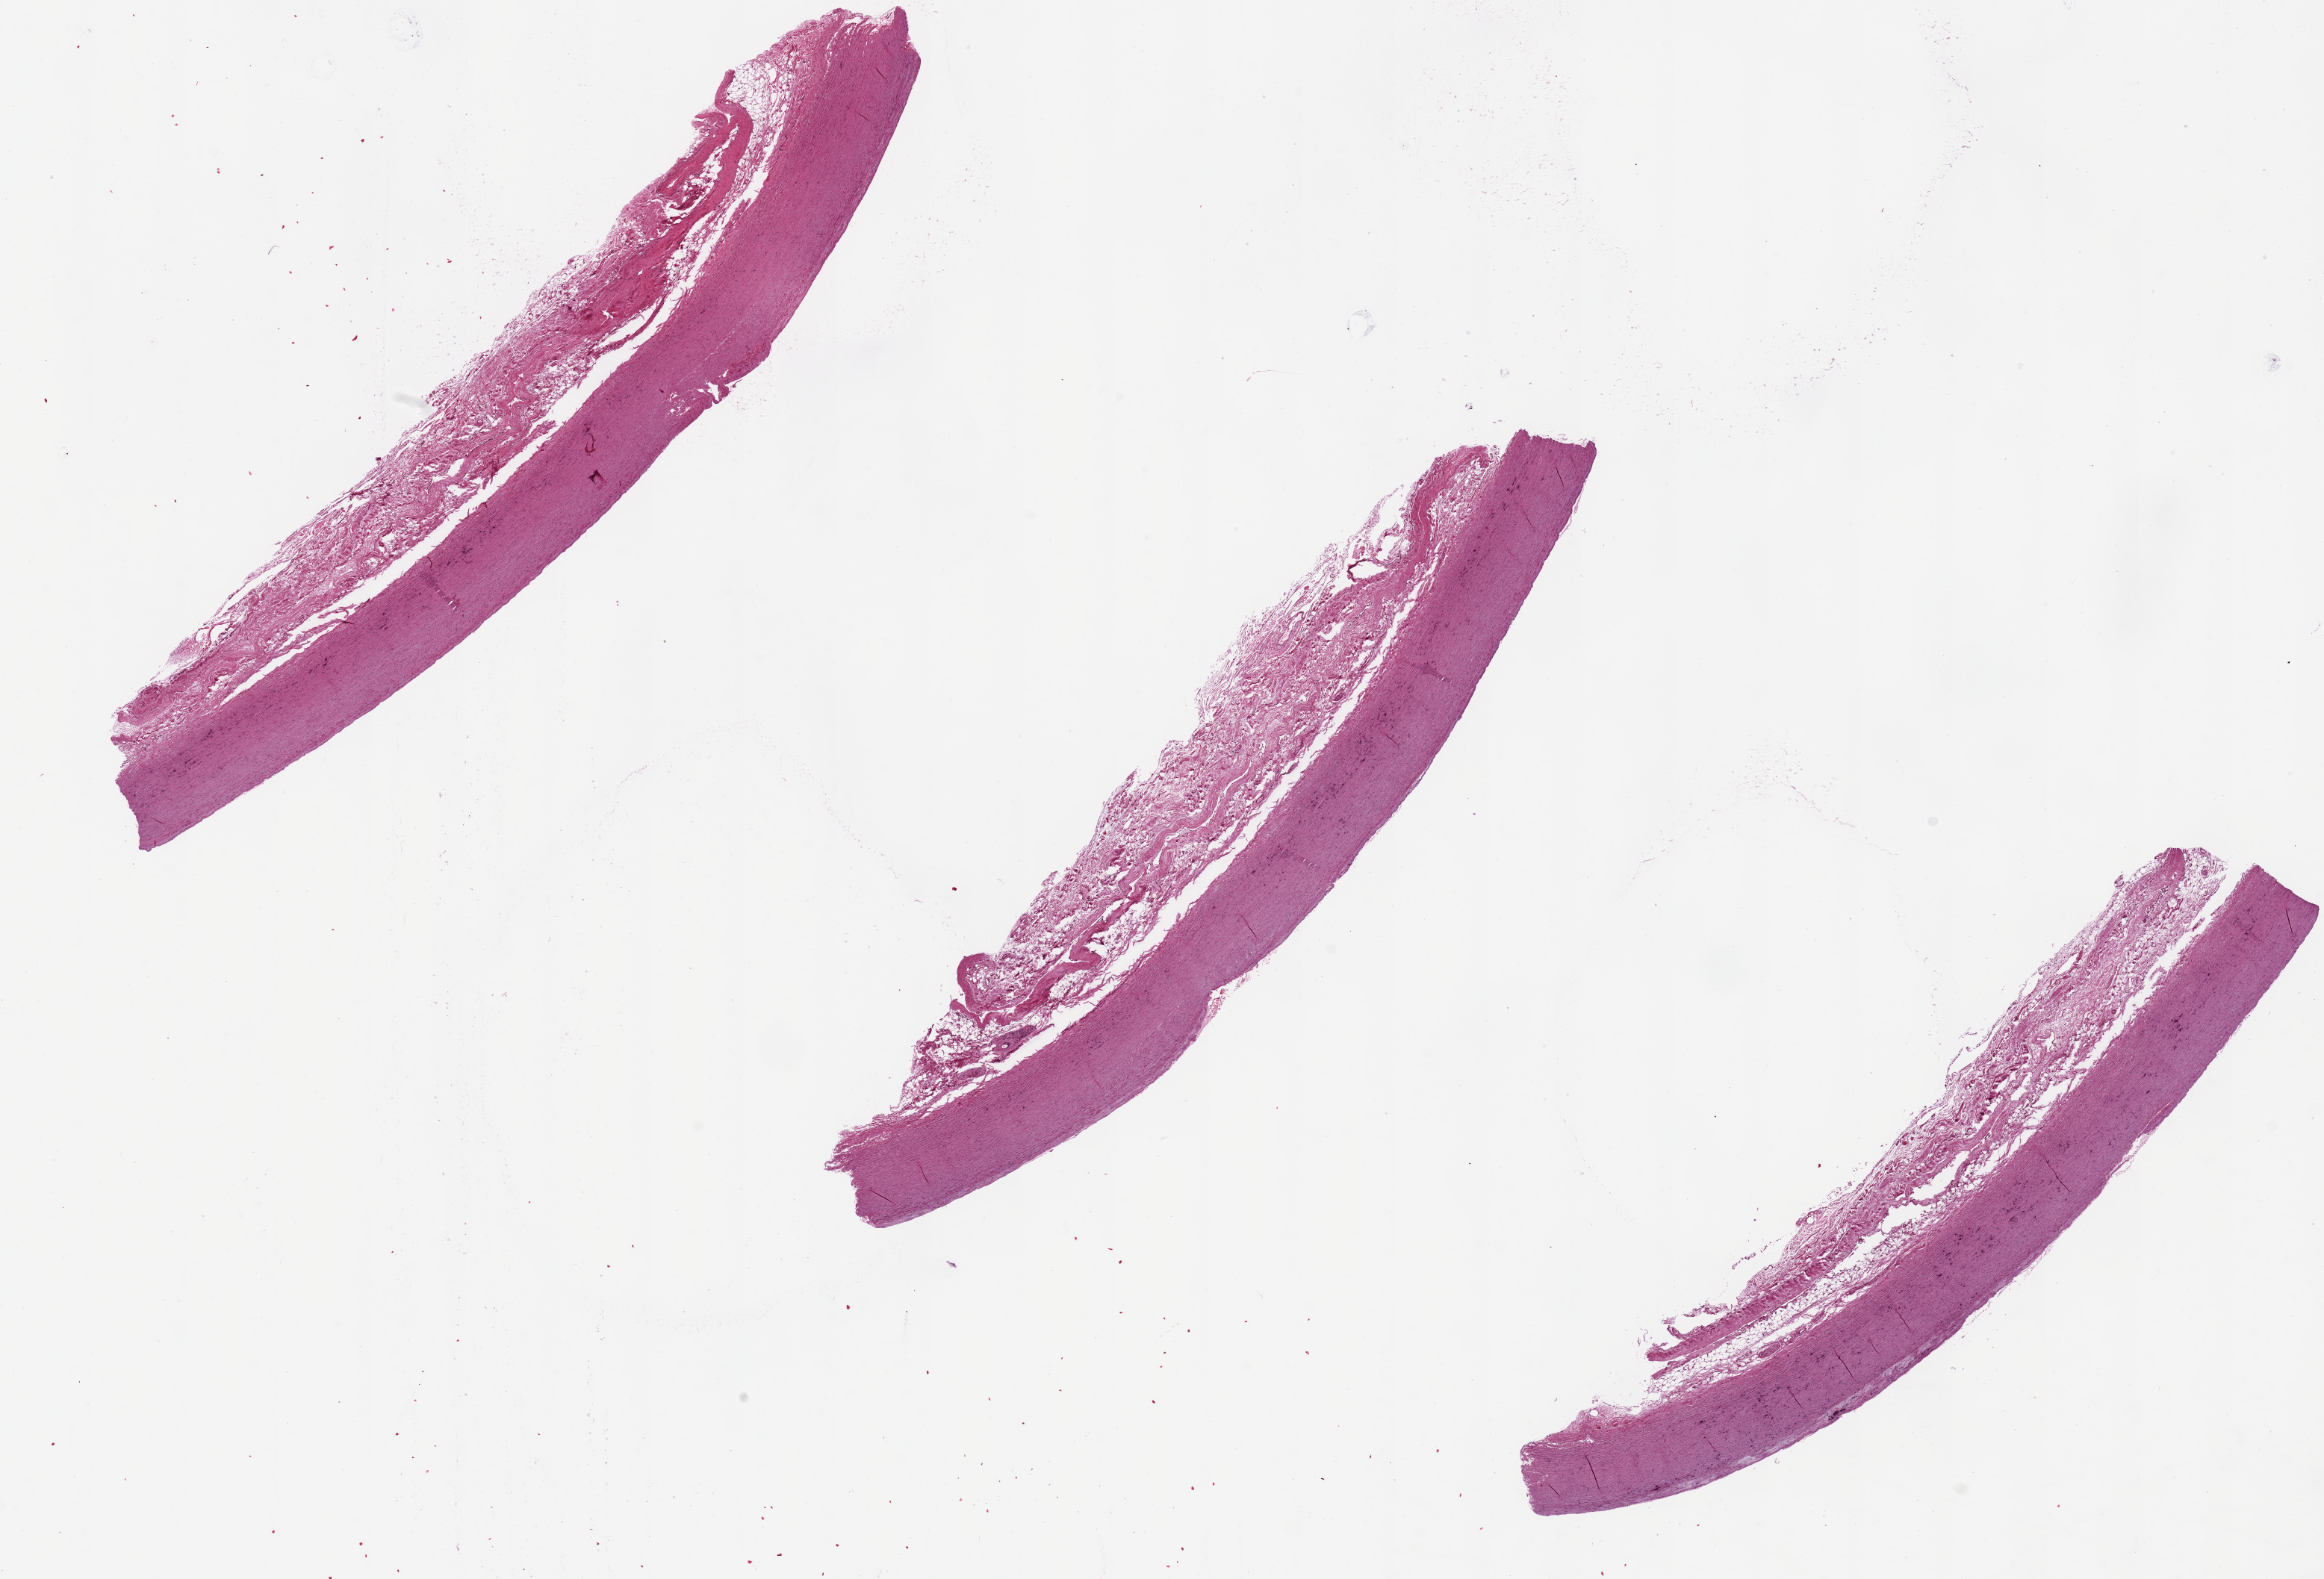
Whole-slide image, hematoxylin and eosin (H&E) stain — shown as a low-resolution overview of the whole scanned area (about 24.6 x 16.7 mm, from a 20x scan), PAXgene-fixed paraffin-embedded (PFPE) section, section of aorta (target tissue), tissue donor sample. Donor: female.
Review note (as recorded): Minimal atherosis; artery is ~42% of thickness of specimen (rest is peri-aortic connective tissues).